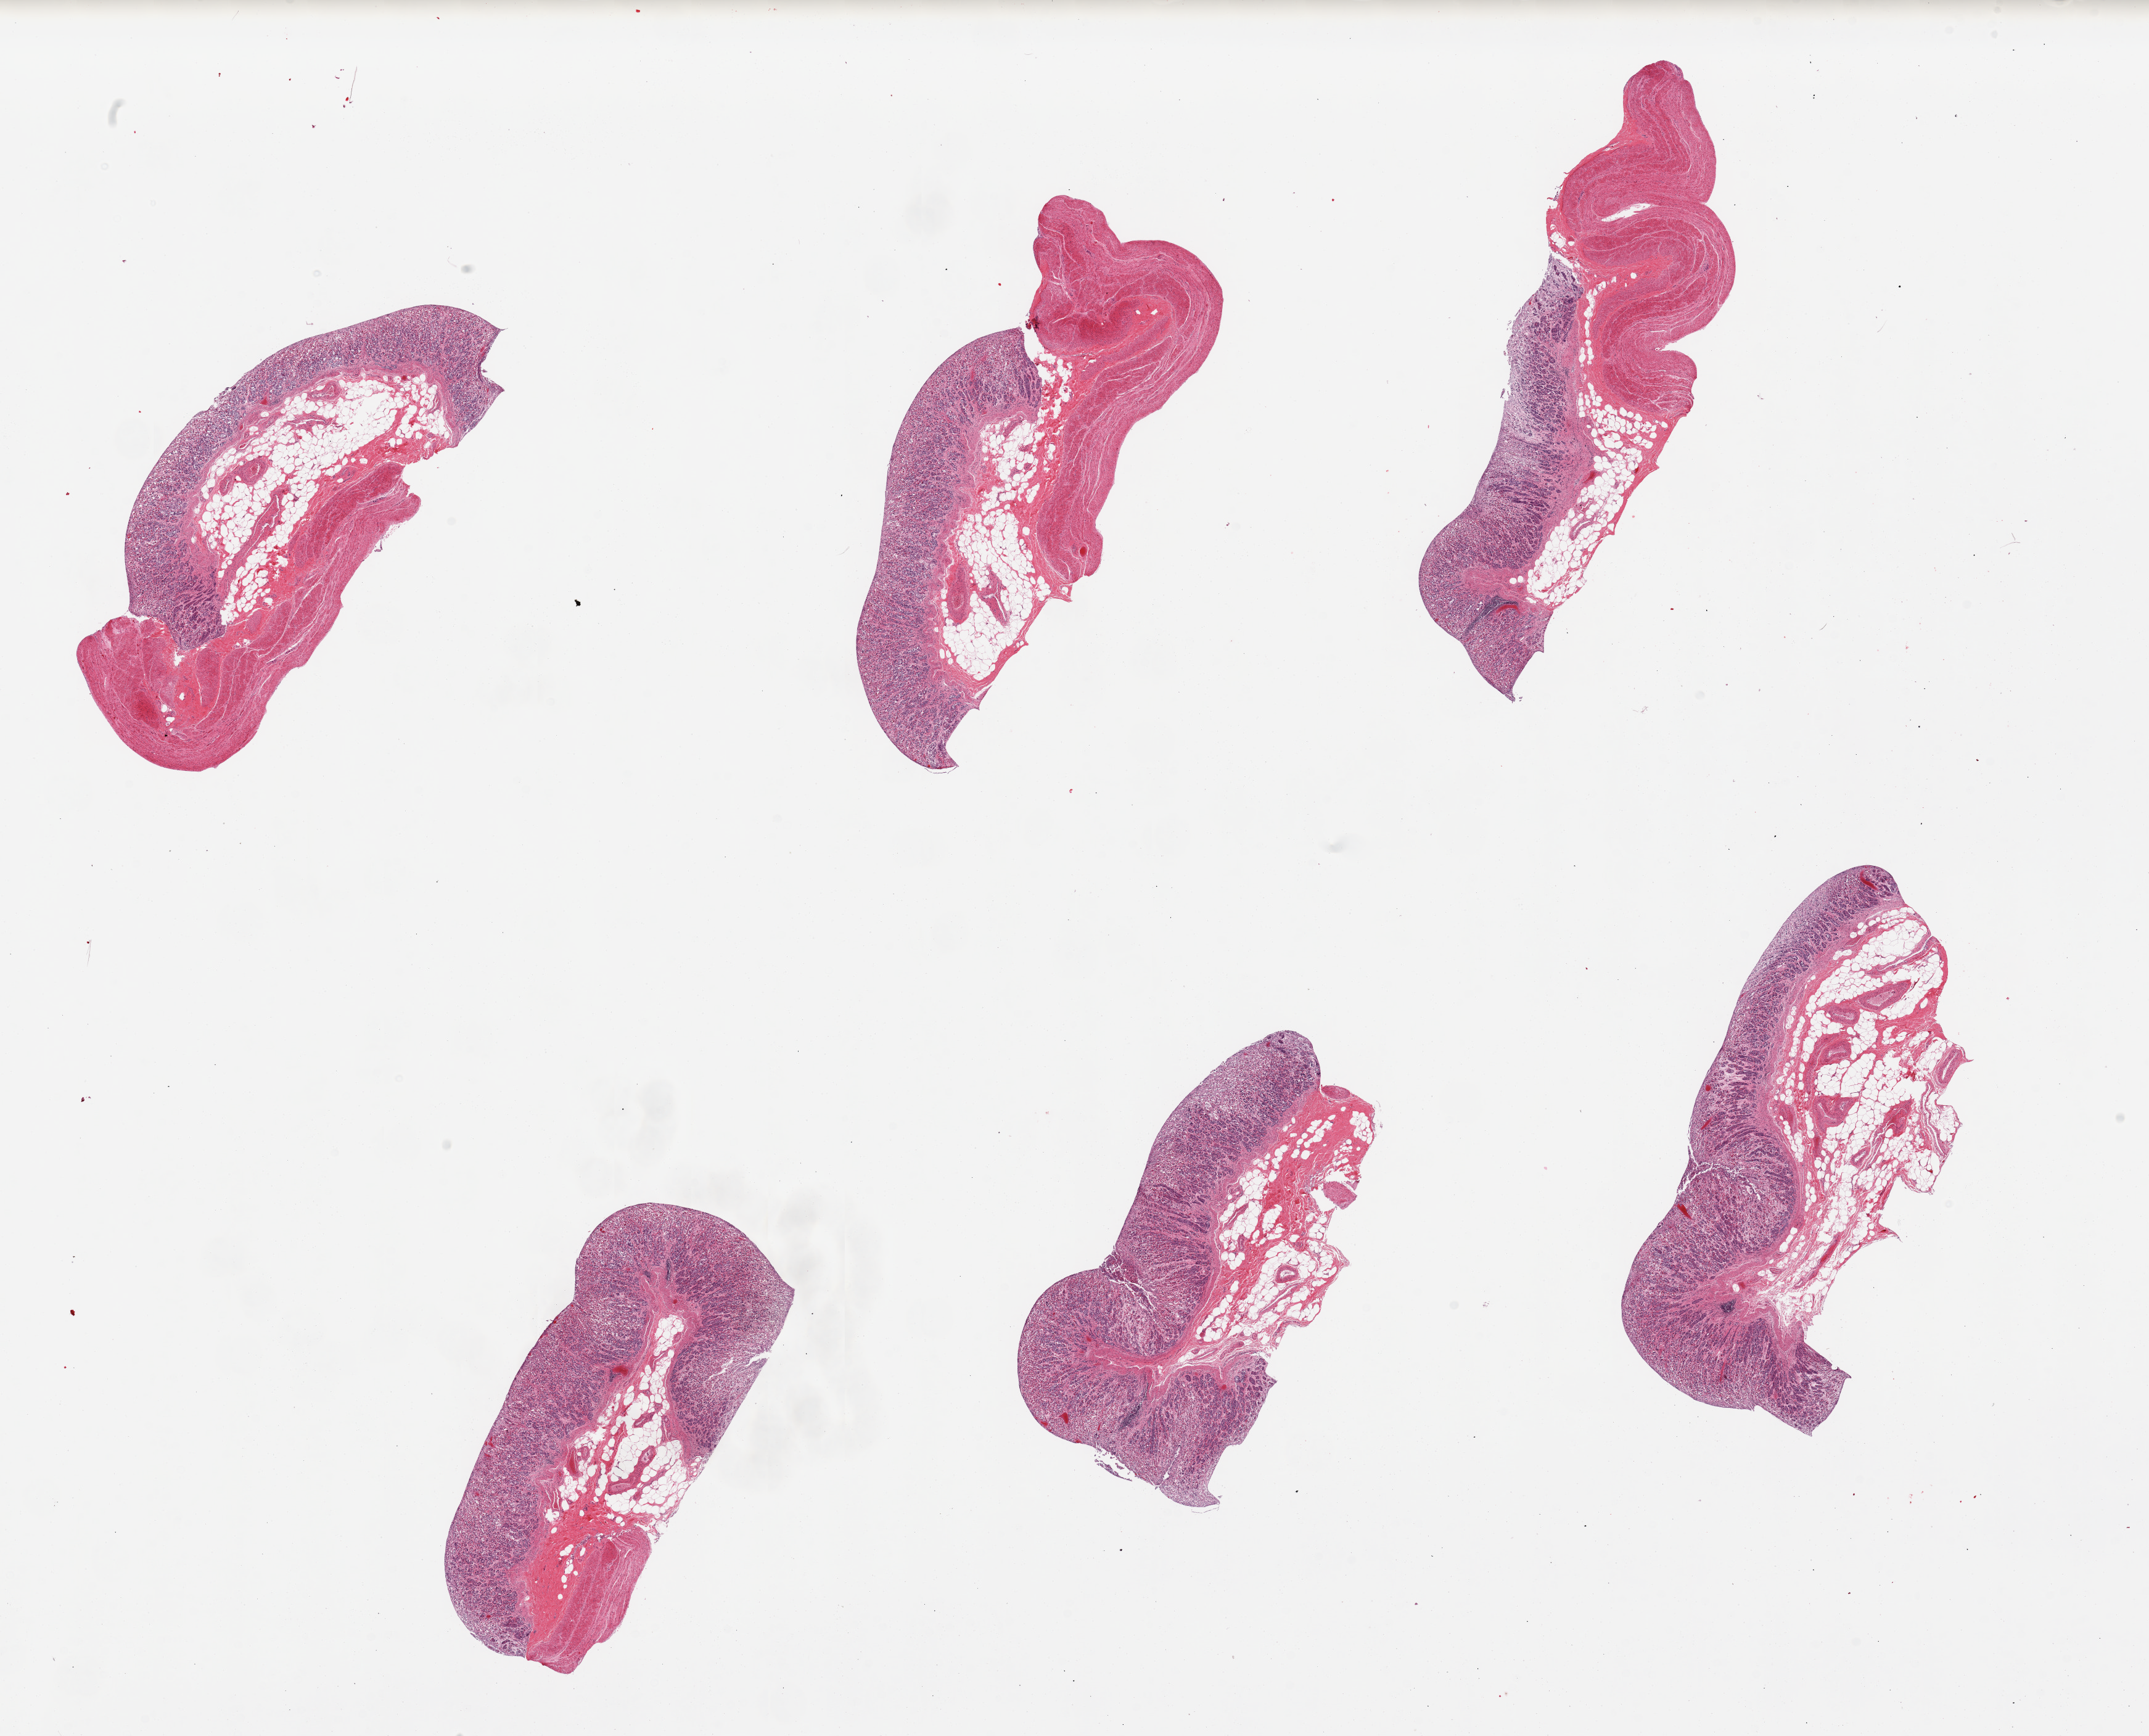
Digitized hematoxylin and eosin (H&E)-stained section — whole scanned area (about 27.6 x 22.3 mm) shown as a low-resolution overview; PAXgene-fixed paraffin-embedded (PFPE) section; target tissue: stomach; donor tissue sample. Donor sex: male.
Review note (as recorded): 6 pieces. 4 have and 2 have not muscularis propria.